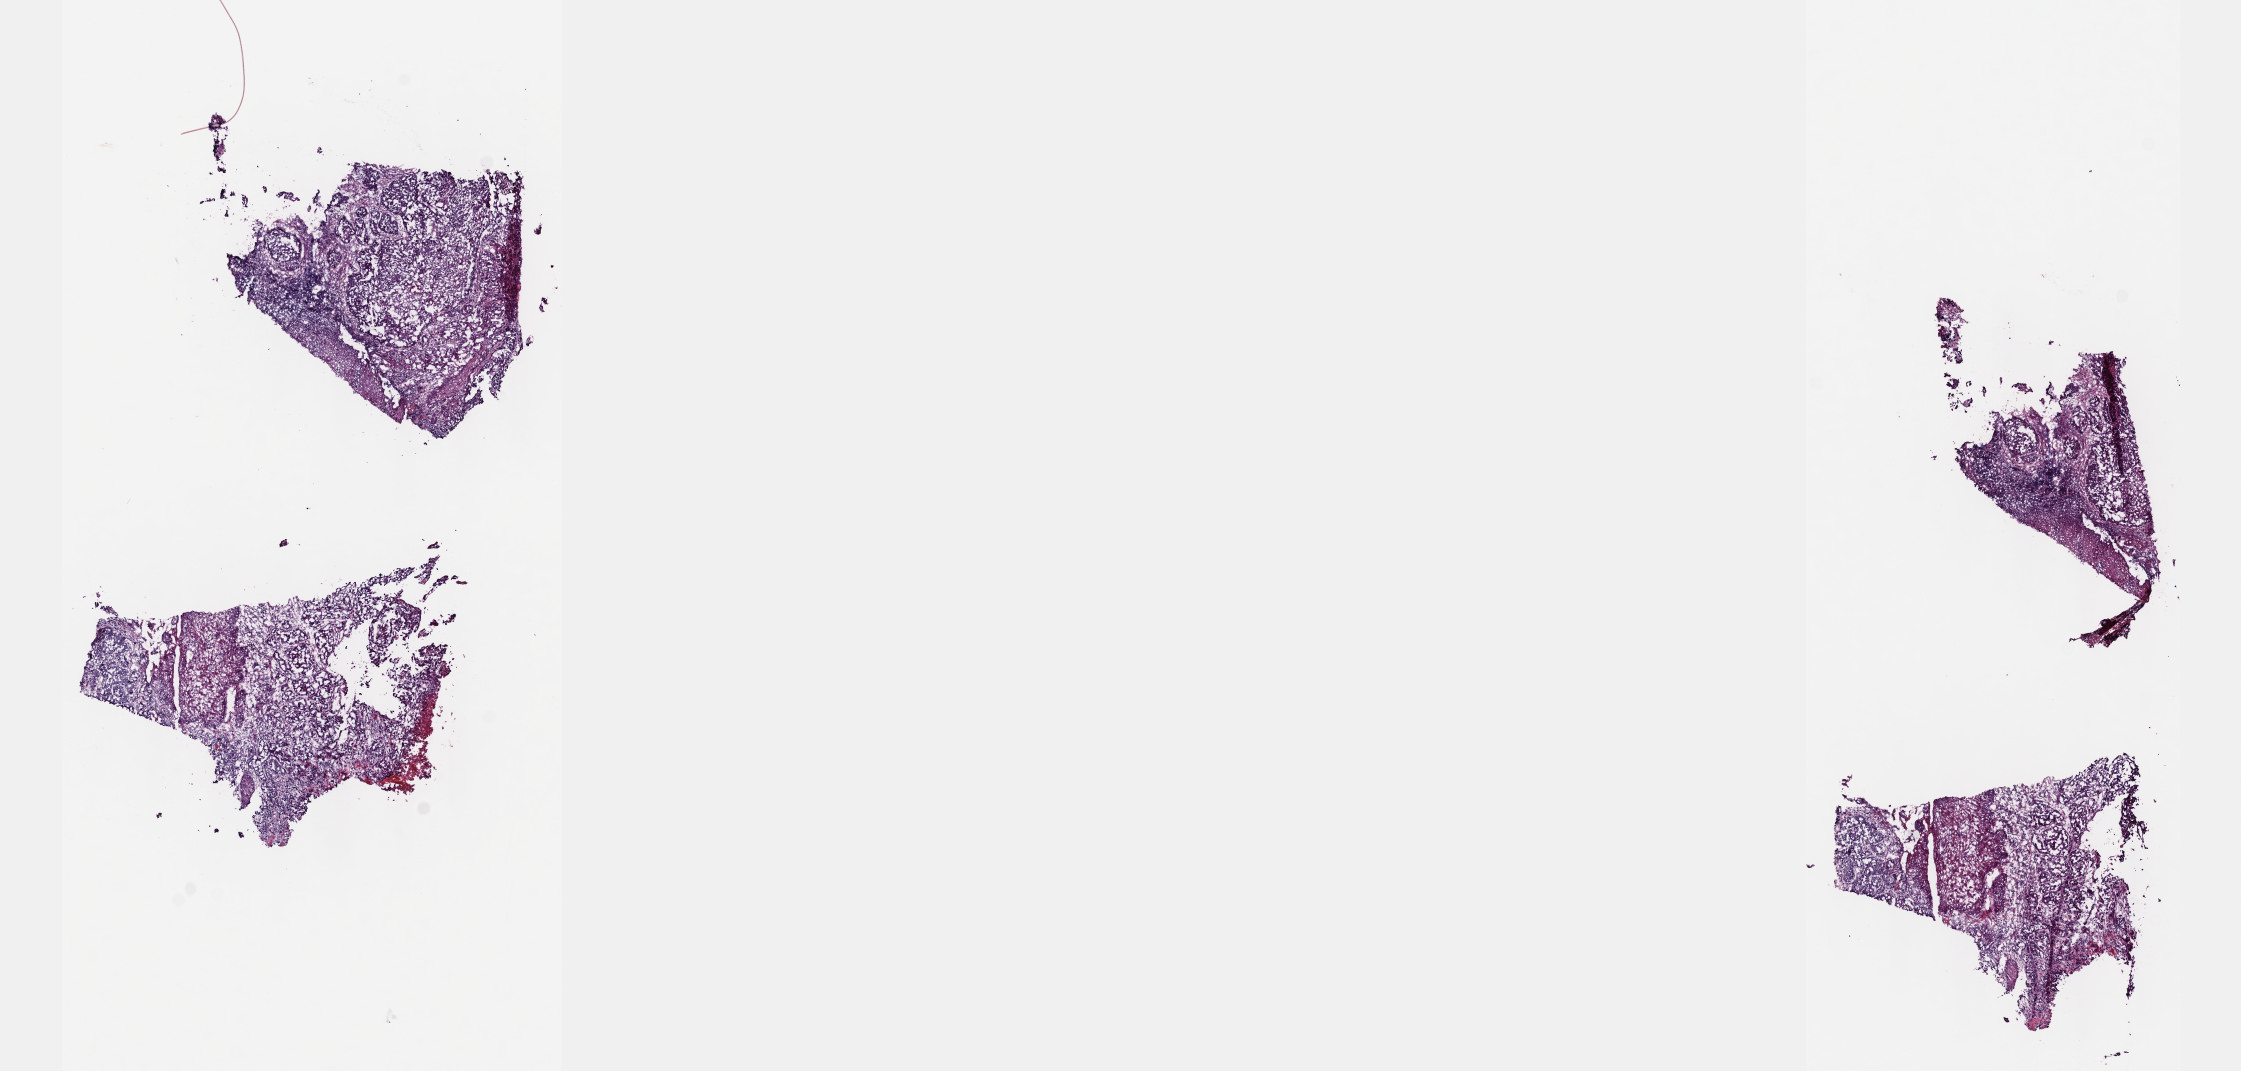
H&E-stained whole-slide image — low-resolution overview of the scanned area, about 18.1 x 8.7 mm (acquisition: 40x scan); frozen section from the top of the tissue portion; sample: primary tumour, head and neck. Male, age 51 years at initial diagnosis. Slide review estimates, as recorded: tumour cells 70%, tumour nuclei 75%, normal cells 10%, stromal cells 20%, necrosis 0%. Infiltration values recorded for this section: lymphocyte infiltration 10%, monocyte infiltration 0%, neutrophil infiltration 0%.
* histologic diagnosis: Squamous cell carcinoma, NOS (base of tongue, NOS)
* laterality: right
* AJCC pathologic stage: IVA (7th edition)